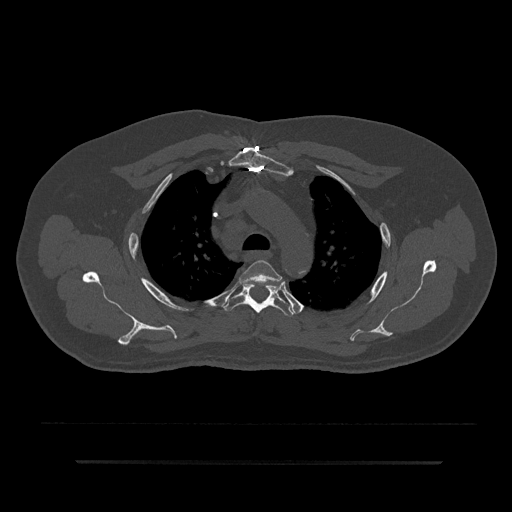
CT including the spine, one axial slice; reconstruction kernel Br40s/3; 120 kVp; bone window (W 1800 / L 400 HU); 0.5 mm slice thickness; 512 × 512 image matrix, field of view 464 × 464 mm. Patient: male, 59 years. From the clinical record (not read from this slice): primary cancer: bile ducts; vertebrae with lytic lesions (as recorded): T10.
Outlined on this slice (semi-automatically segmented with operator editing):
- T3 vertebra: box from (x=239, y=260) to (x=283, y=284) px
- T4 vertebra: (x=222, y=283)–(x=294, y=316)